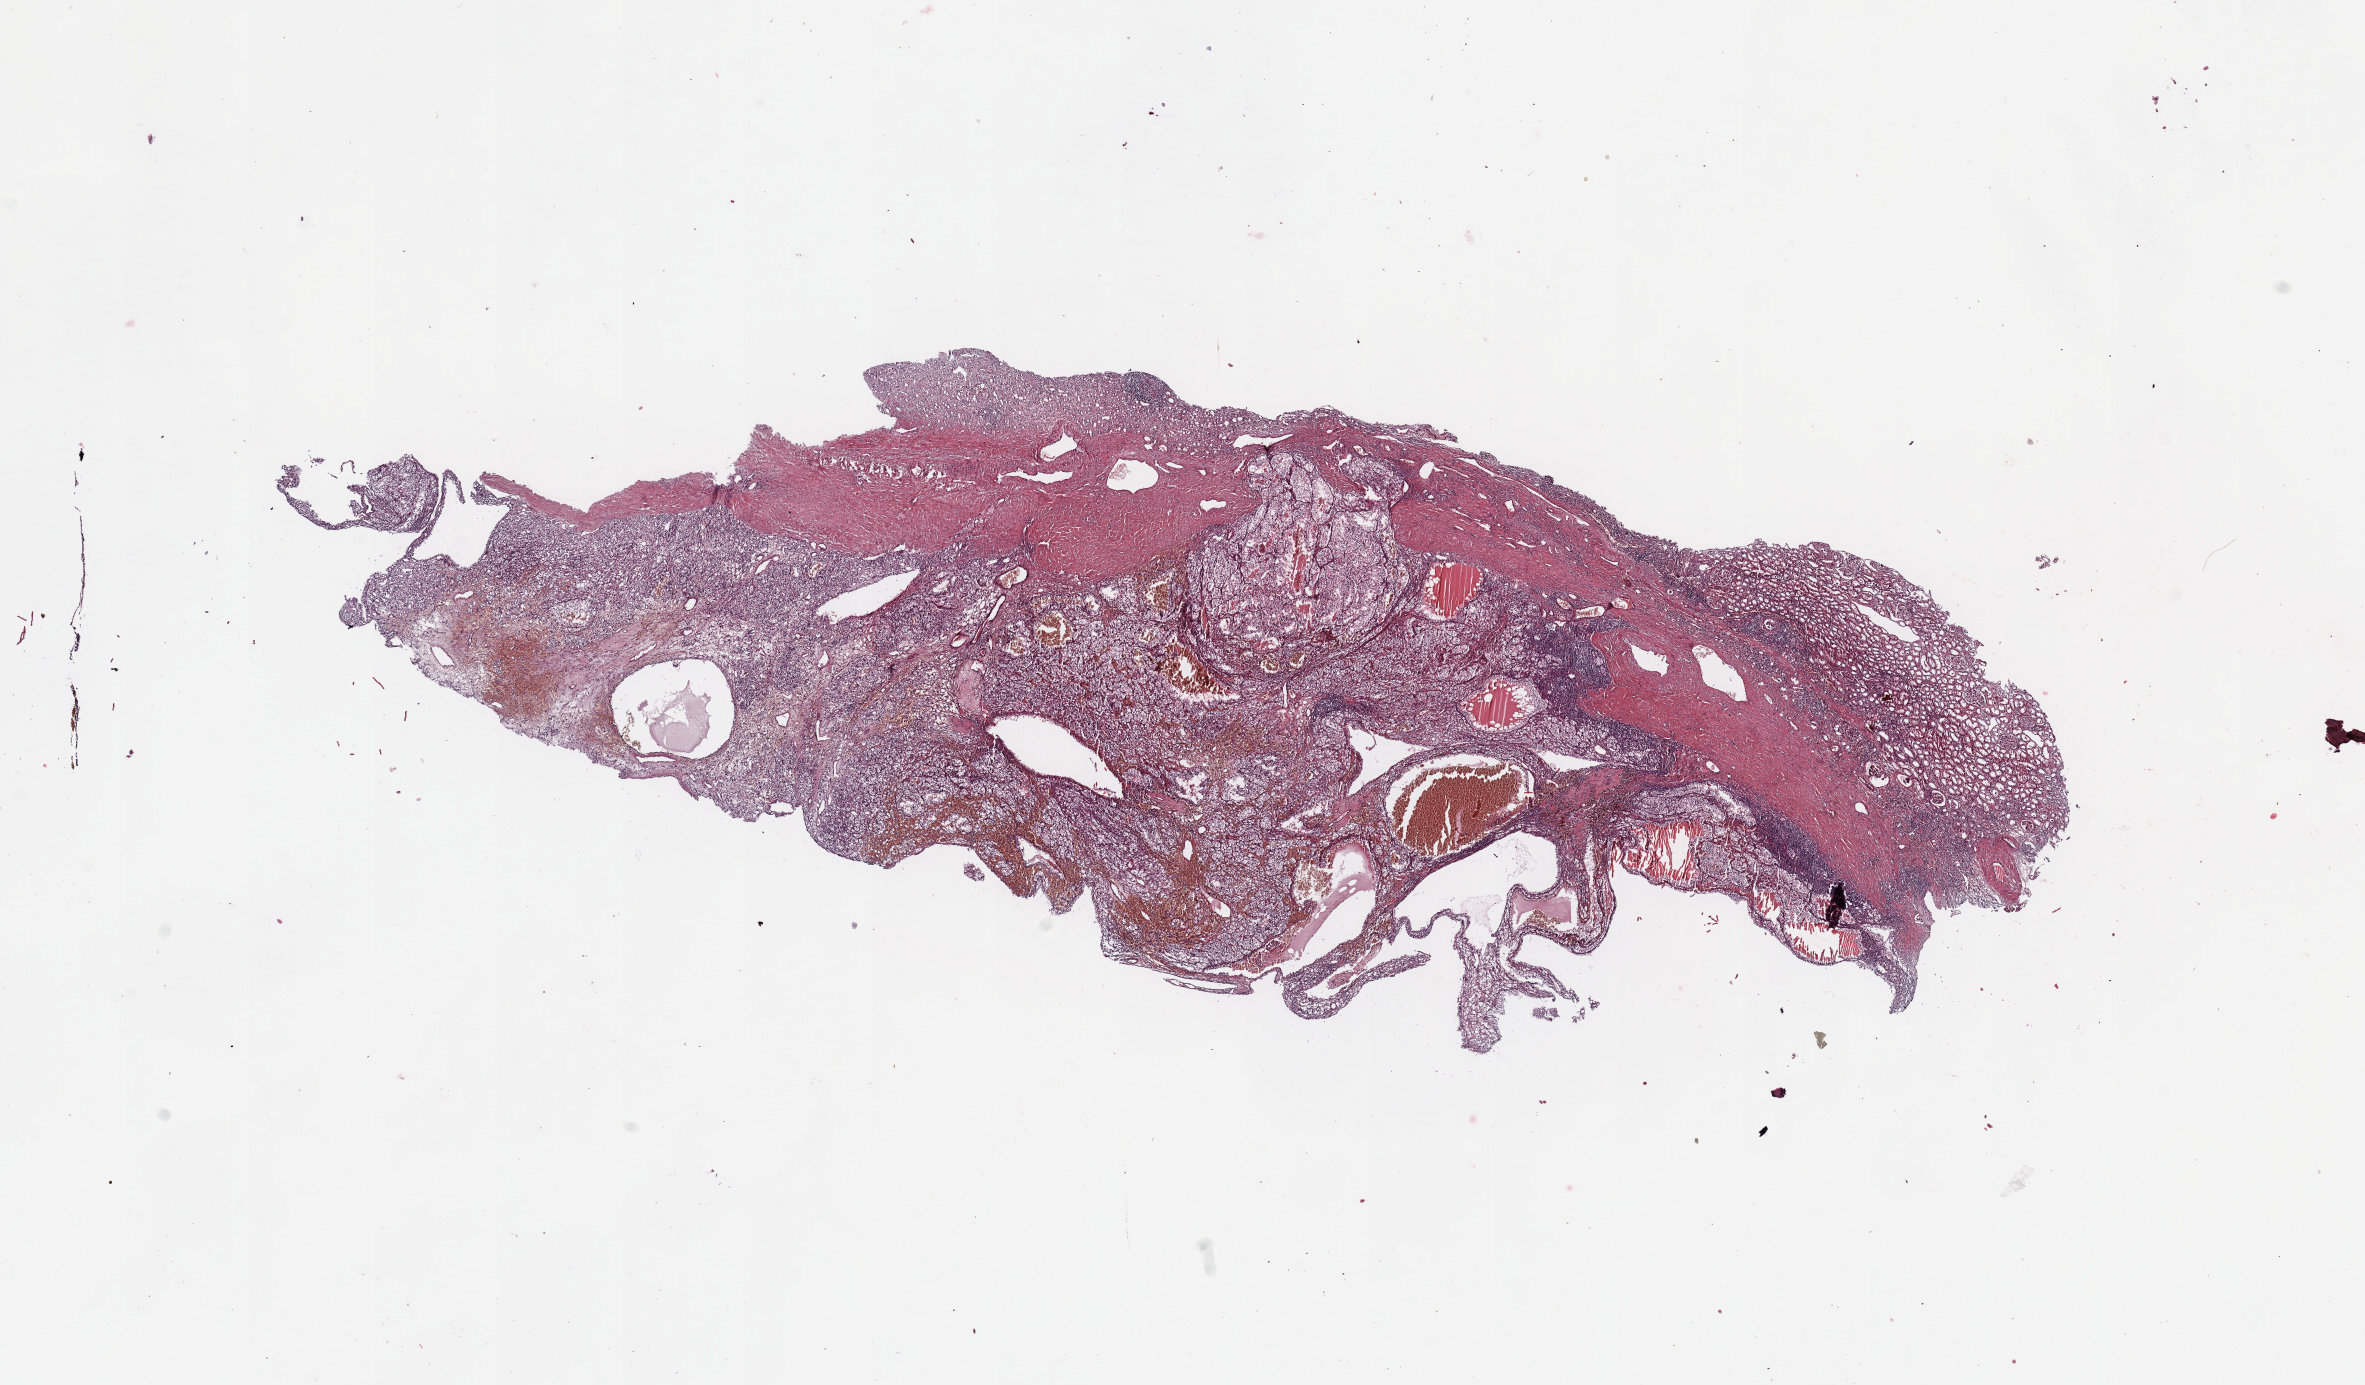
Whole-slide histology image, H&E — whole scanned area (about 18.7 x 11.0 mm) shown as a low-resolution overview. Tumour tissue sample, kidney. Patient: male, age 49 years. Histologic grade: G2 (moderately differentiated).
Primary tumour site (as recorded): upper pole. Diagnosis: Renal cell carcinoma, NOS. AJCC pathologic stage: I.